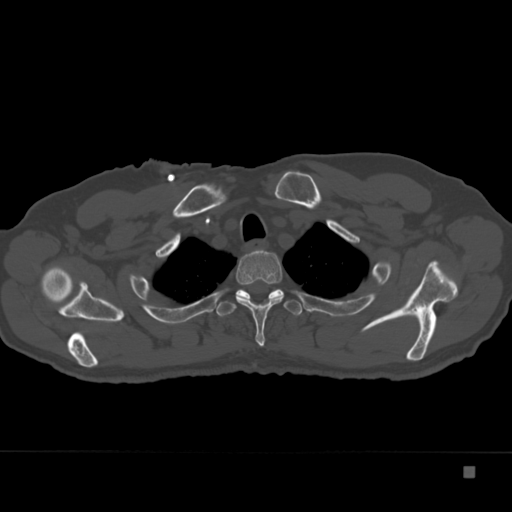
CT including the spine, one axial slice. Position 296 of 332 along the scan axis. Reconstruction kernel Br40s. Bone window (W 1800 / L 400 HU). 1.5 mm slice thickness. 512 × 512 image matrix. Patient: male, 72 years. From the clinical record (not read from this slice): primary cancer: skeletal.
Structures marked on this image (semi-automatically segmented with operator editing):
- T2 vertebra: bounding box <236,250,284,347> (left, top, right, bottom; pixels)
- T3 vertebra: <216,289,303,317>